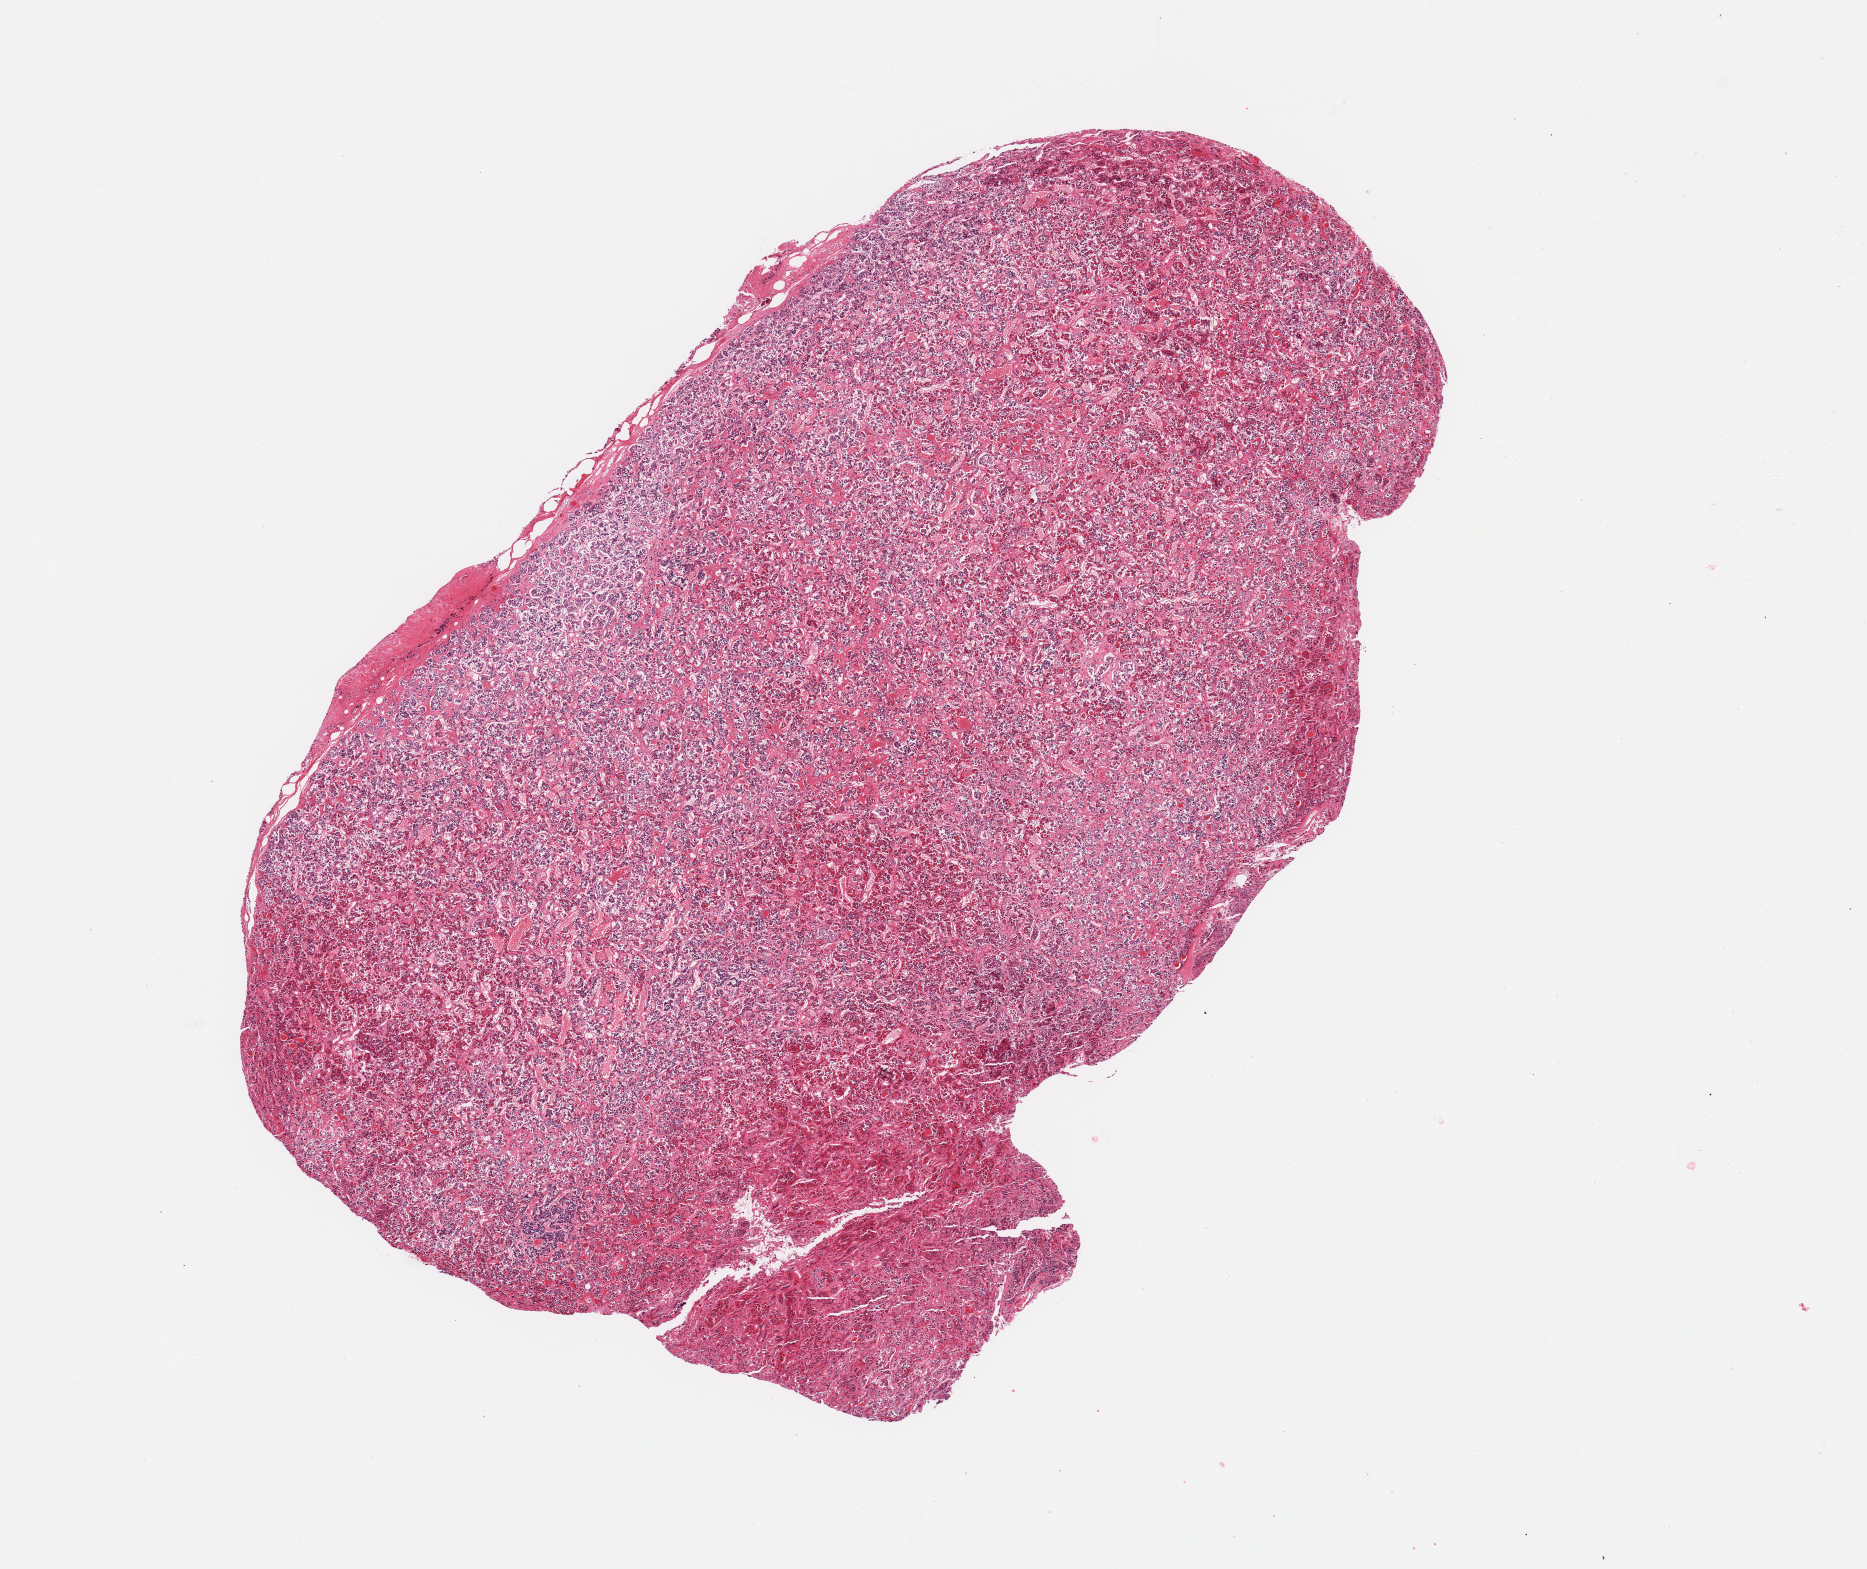
H&E whole-slide image, shown as a low-resolution overview of the whole scanned area (about 14.8 x 12.4 mm), PAXgene-fixed paraffin-embedded (PFPE) section, target tissue: pituitary, tissue donor sample. Donor sex: male.
* reviewer comment on this tissue sample: 1 piece; all adenohypophysis; no neural component